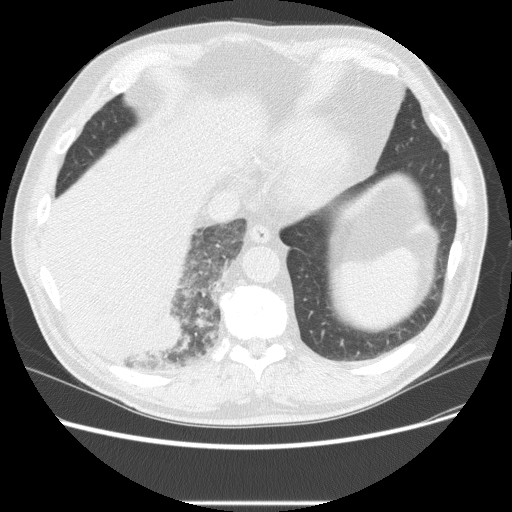
Low-dose screening chest CT, one axial slice; position 55 of 233 along the scan axis; lung window (W 1500 / L -600 HU); 2.5 mm slice thickness; 512 × 512 image matrix, field of view 380 × 380 mm.
Annotated regions visible in this slice (manually delineated by an expert):
- lesion 3 (tumor, lower lobe of right lung): bounding box [x1, y1, x2, y2] px = [65, 299, 179, 365]